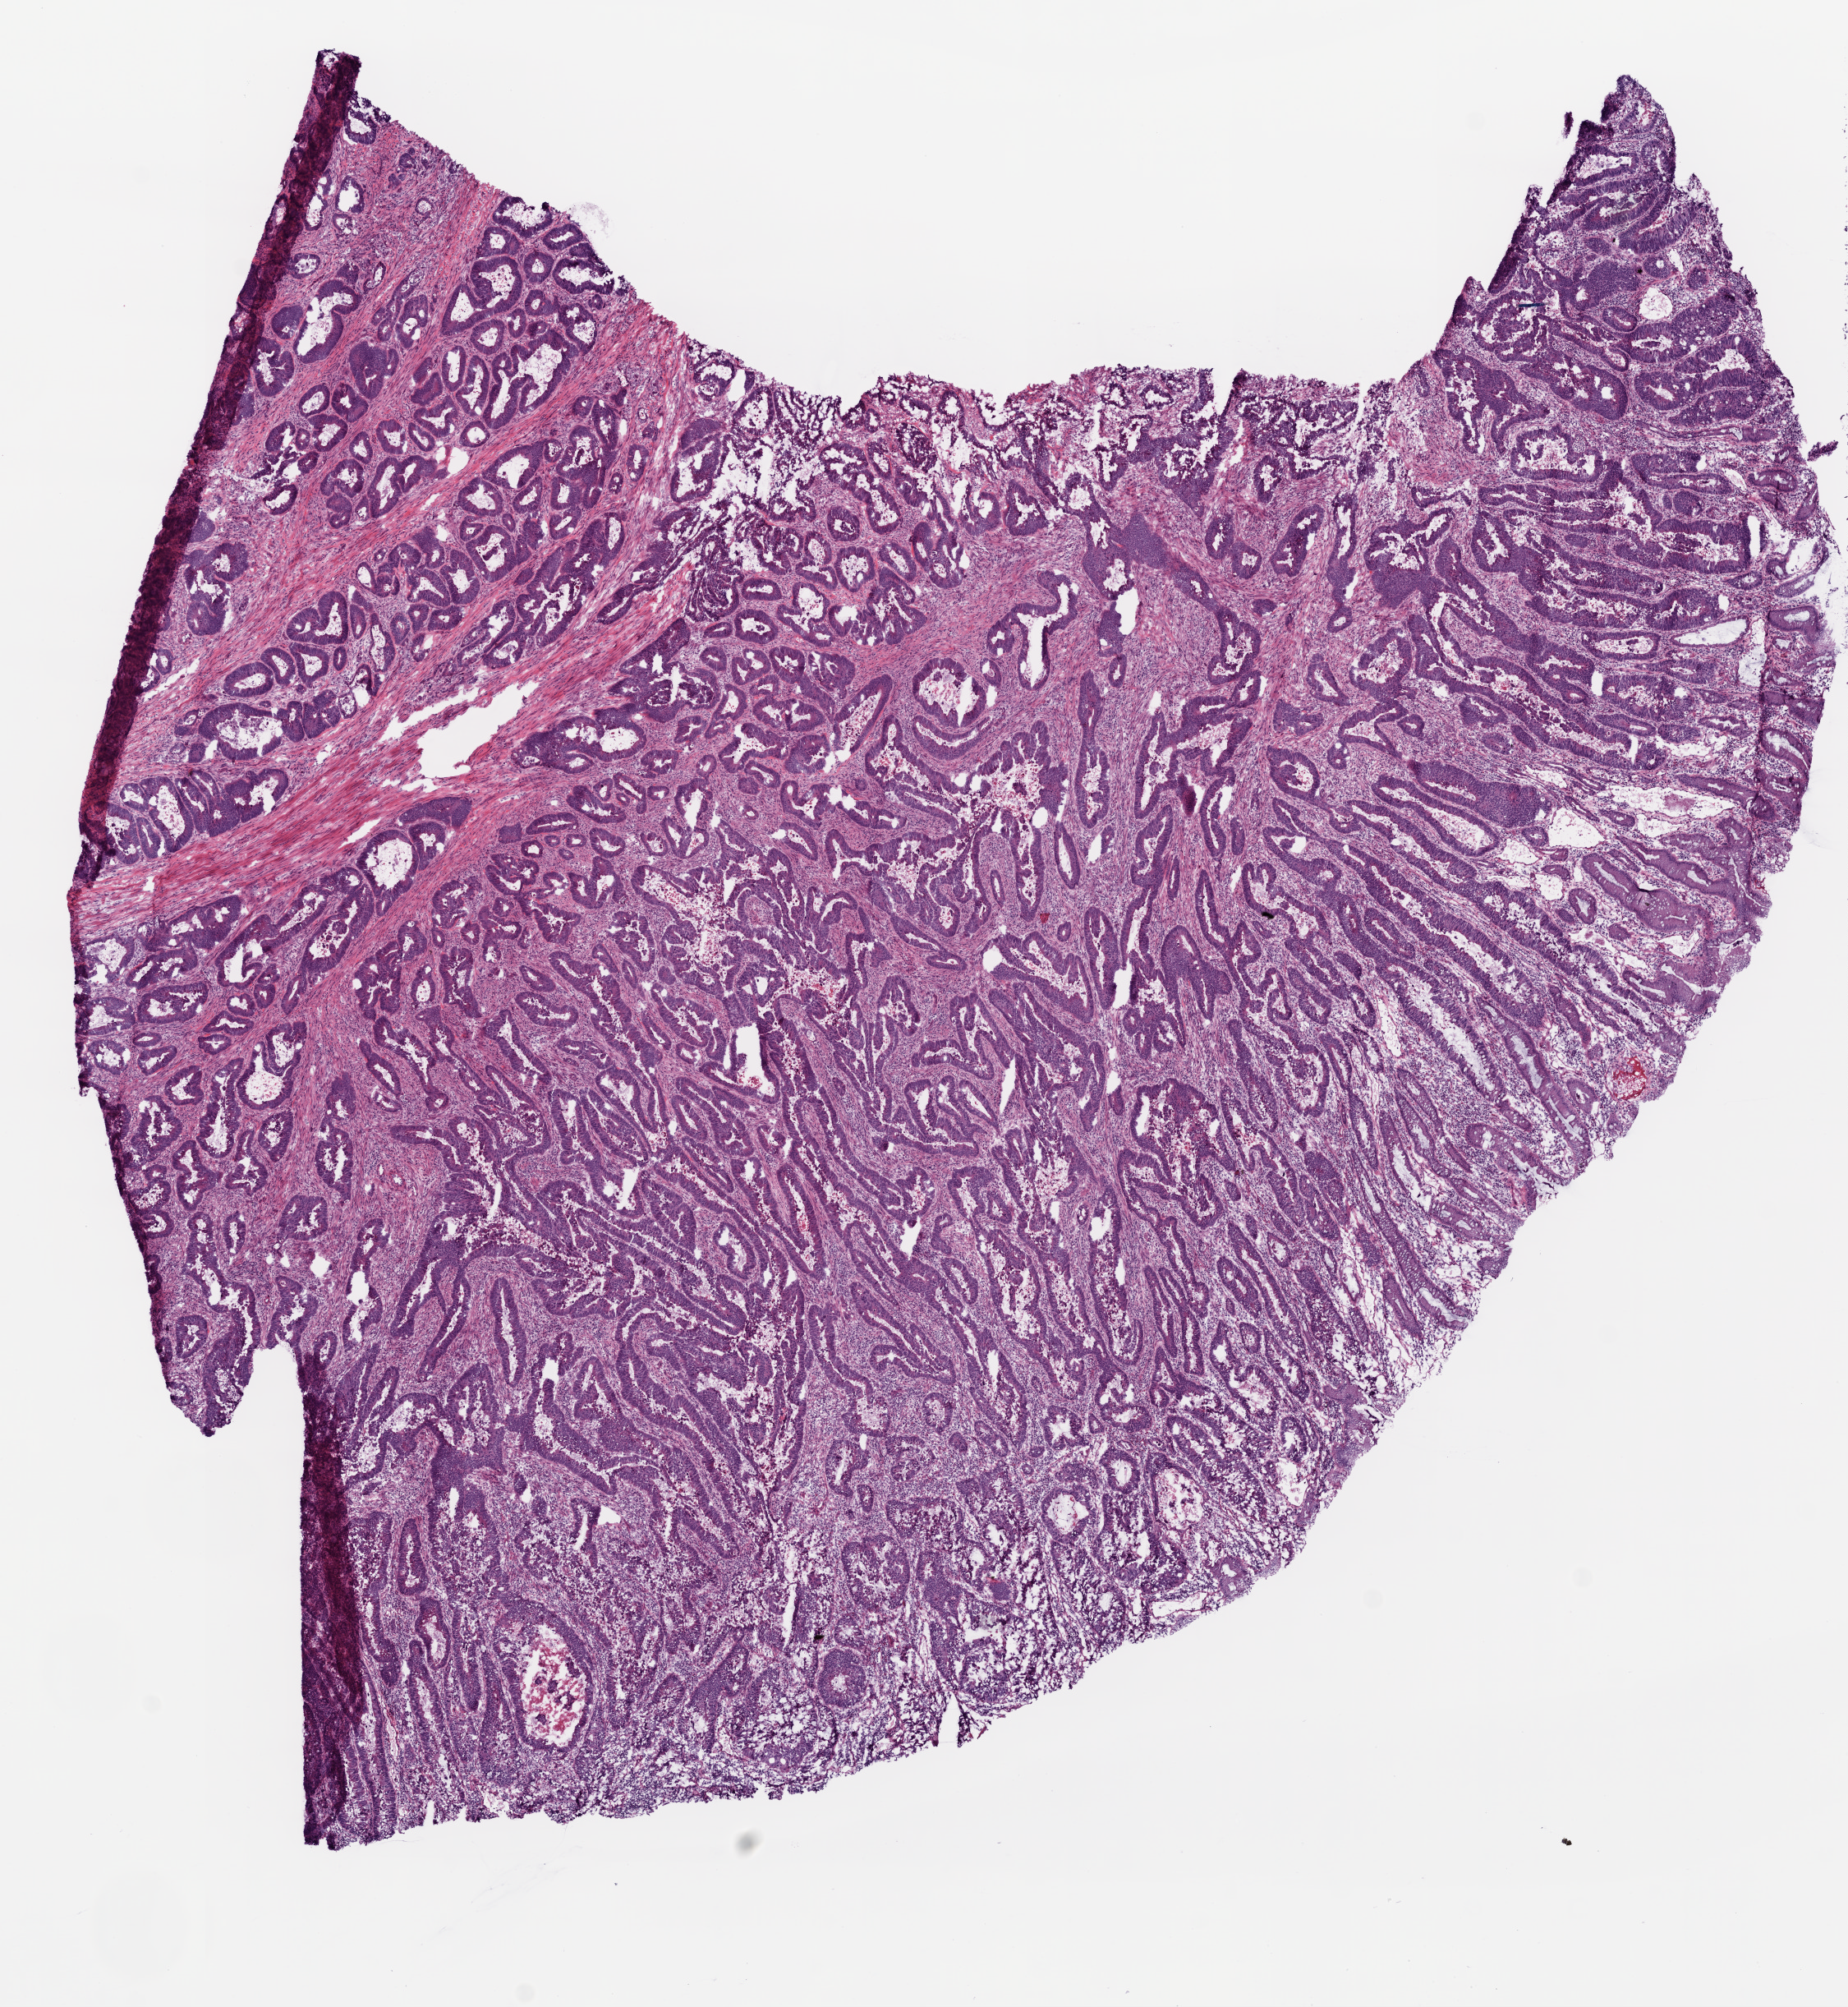
Digitized H&E tissue section (whole slide), shown as a low-resolution overview of the whole scanned area (about 9.0 x 9.8 mm, acquisition: 20x scan). Frozen section from the bottom of the tissue portion. Rectum, primary tumour sample. Male patient; age at initial diagnosis 86 years. Composition of this section per pathologist review: tumour cells 60%, tumour nuclei 75%, normal cells 25%, stromal cells 10%, necrosis 5%.
Pathologic diagnosis: Adenocarcinoma, NOS. AJCC pathologic stage: IV (6th edition). TNM: T4 N2 M1.